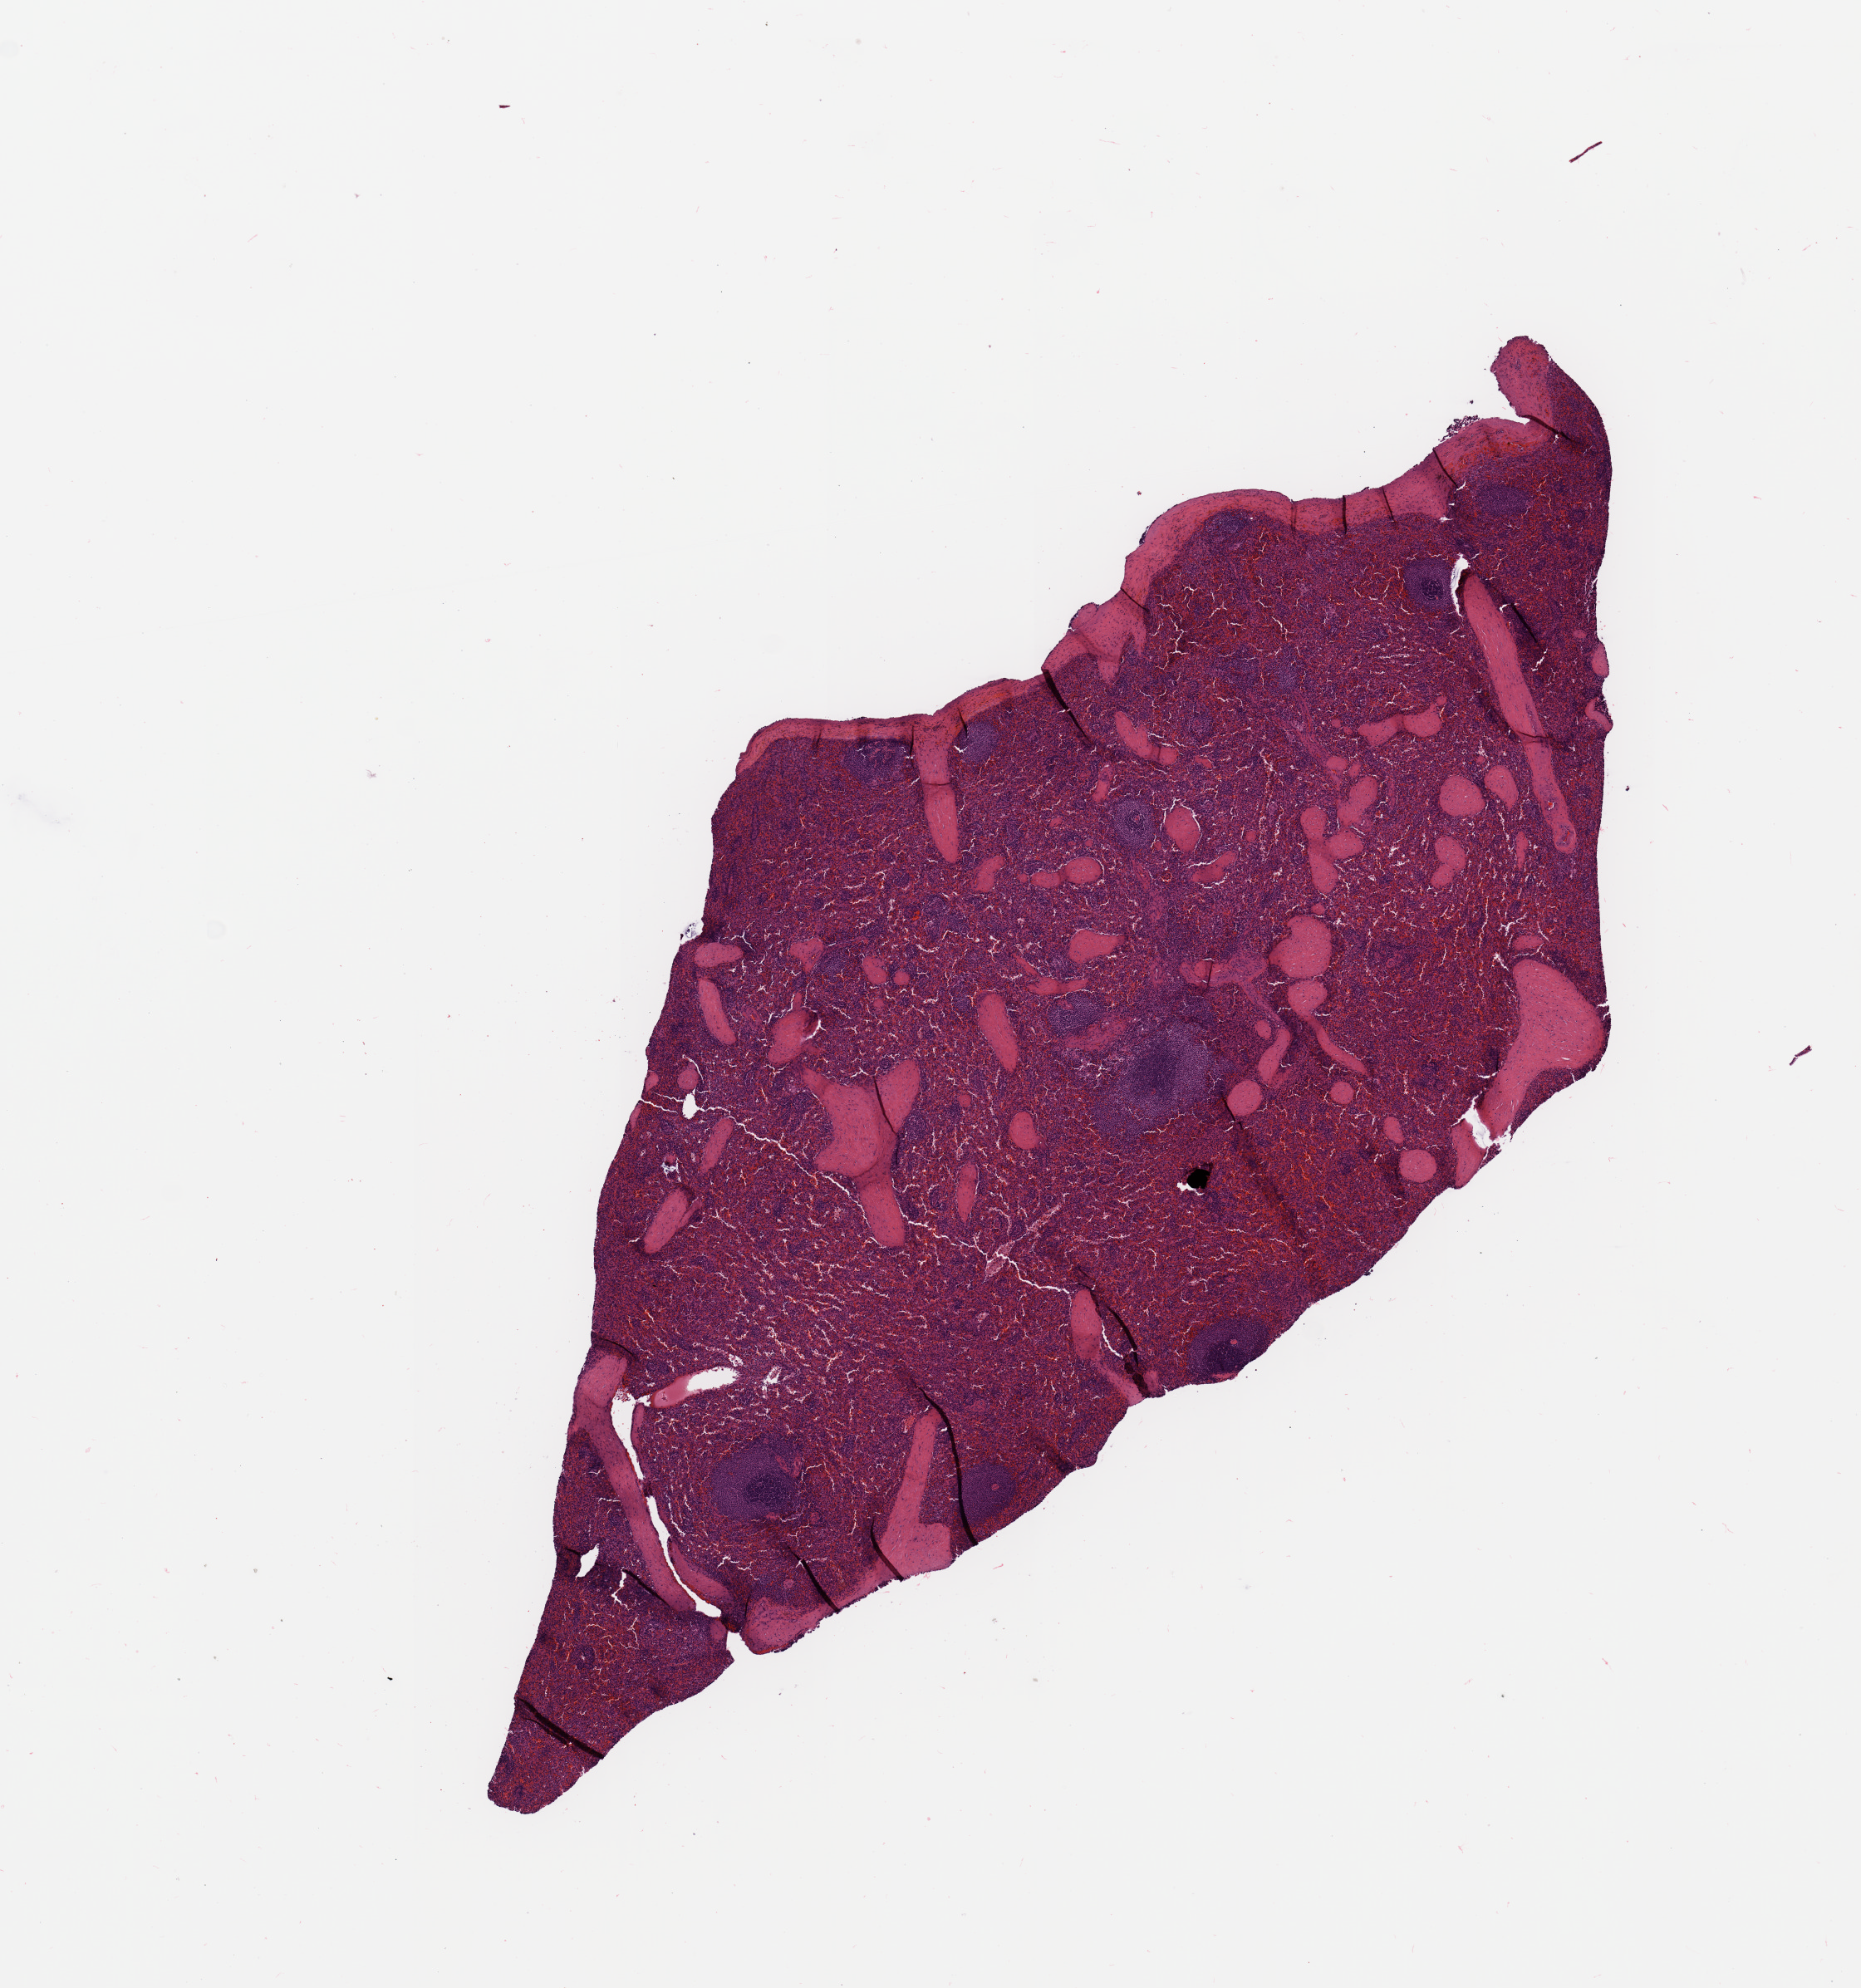
Digitized H&E-stained tissue section (whole slide), low-resolution overview of the scanned area, about 8.9 x 9.5 mm (slide scanned at 20x), normal (non-tumour) tissue sample, pancreas. Patient: male, age 69 years.
This section: normal (non-tumour) tissue from the same patient. Patient diagnosis: Infiltrating duct carcinoma, NOS.